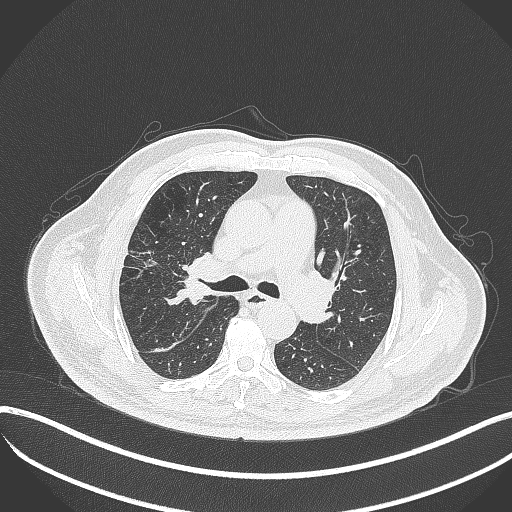
Chest CT, one axial slice. Slice 225 of 401 in the series (ordered by position). Reconstruction kernel B70f. 120 kVp. Lung window (W 1500 / L -600 HU). 512 × 512 image matrix, field of view 400 × 400 mm. Male patient, age 72 years. Case-level facts recorded for this patient, not image findings: clinical TNM (as recorded): T1c N0 M0.
Outlined on this slice (rectangle marked by the reading radiologist):
- lung tumour (recorded histology: squamous cell carcinoma): bounding box [x1, y1, x2, y2] px = [165, 255, 205, 311]